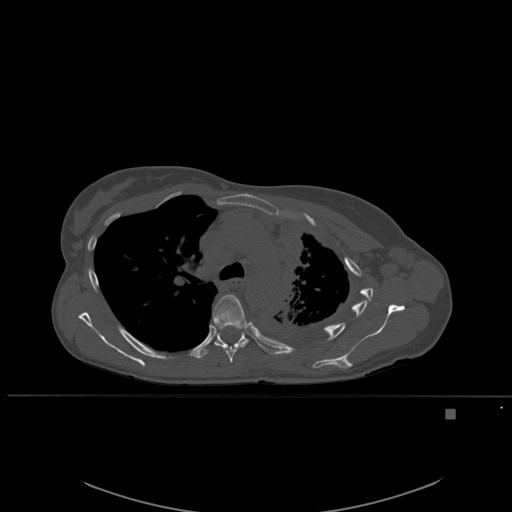
CT including the spine, one axial slice; position 392 of 537 along the scan axis; bone window (W 1800 / L 400 HU); 1.5 mm slice thickness; 512 × 512 image matrix, field of view 440 × 440 mm. Female patient, age 45 years. Case-level facts recorded for this patient, not image findings: primary cancer: lung.
Outlined on this slice (semi-automatic segmentation, software-assisted and operator-edited):
- T5 vertebra: box from (x=213, y=294) to (x=249, y=363) px
- T6 vertebra: (x=196, y=328)–(x=261, y=360)